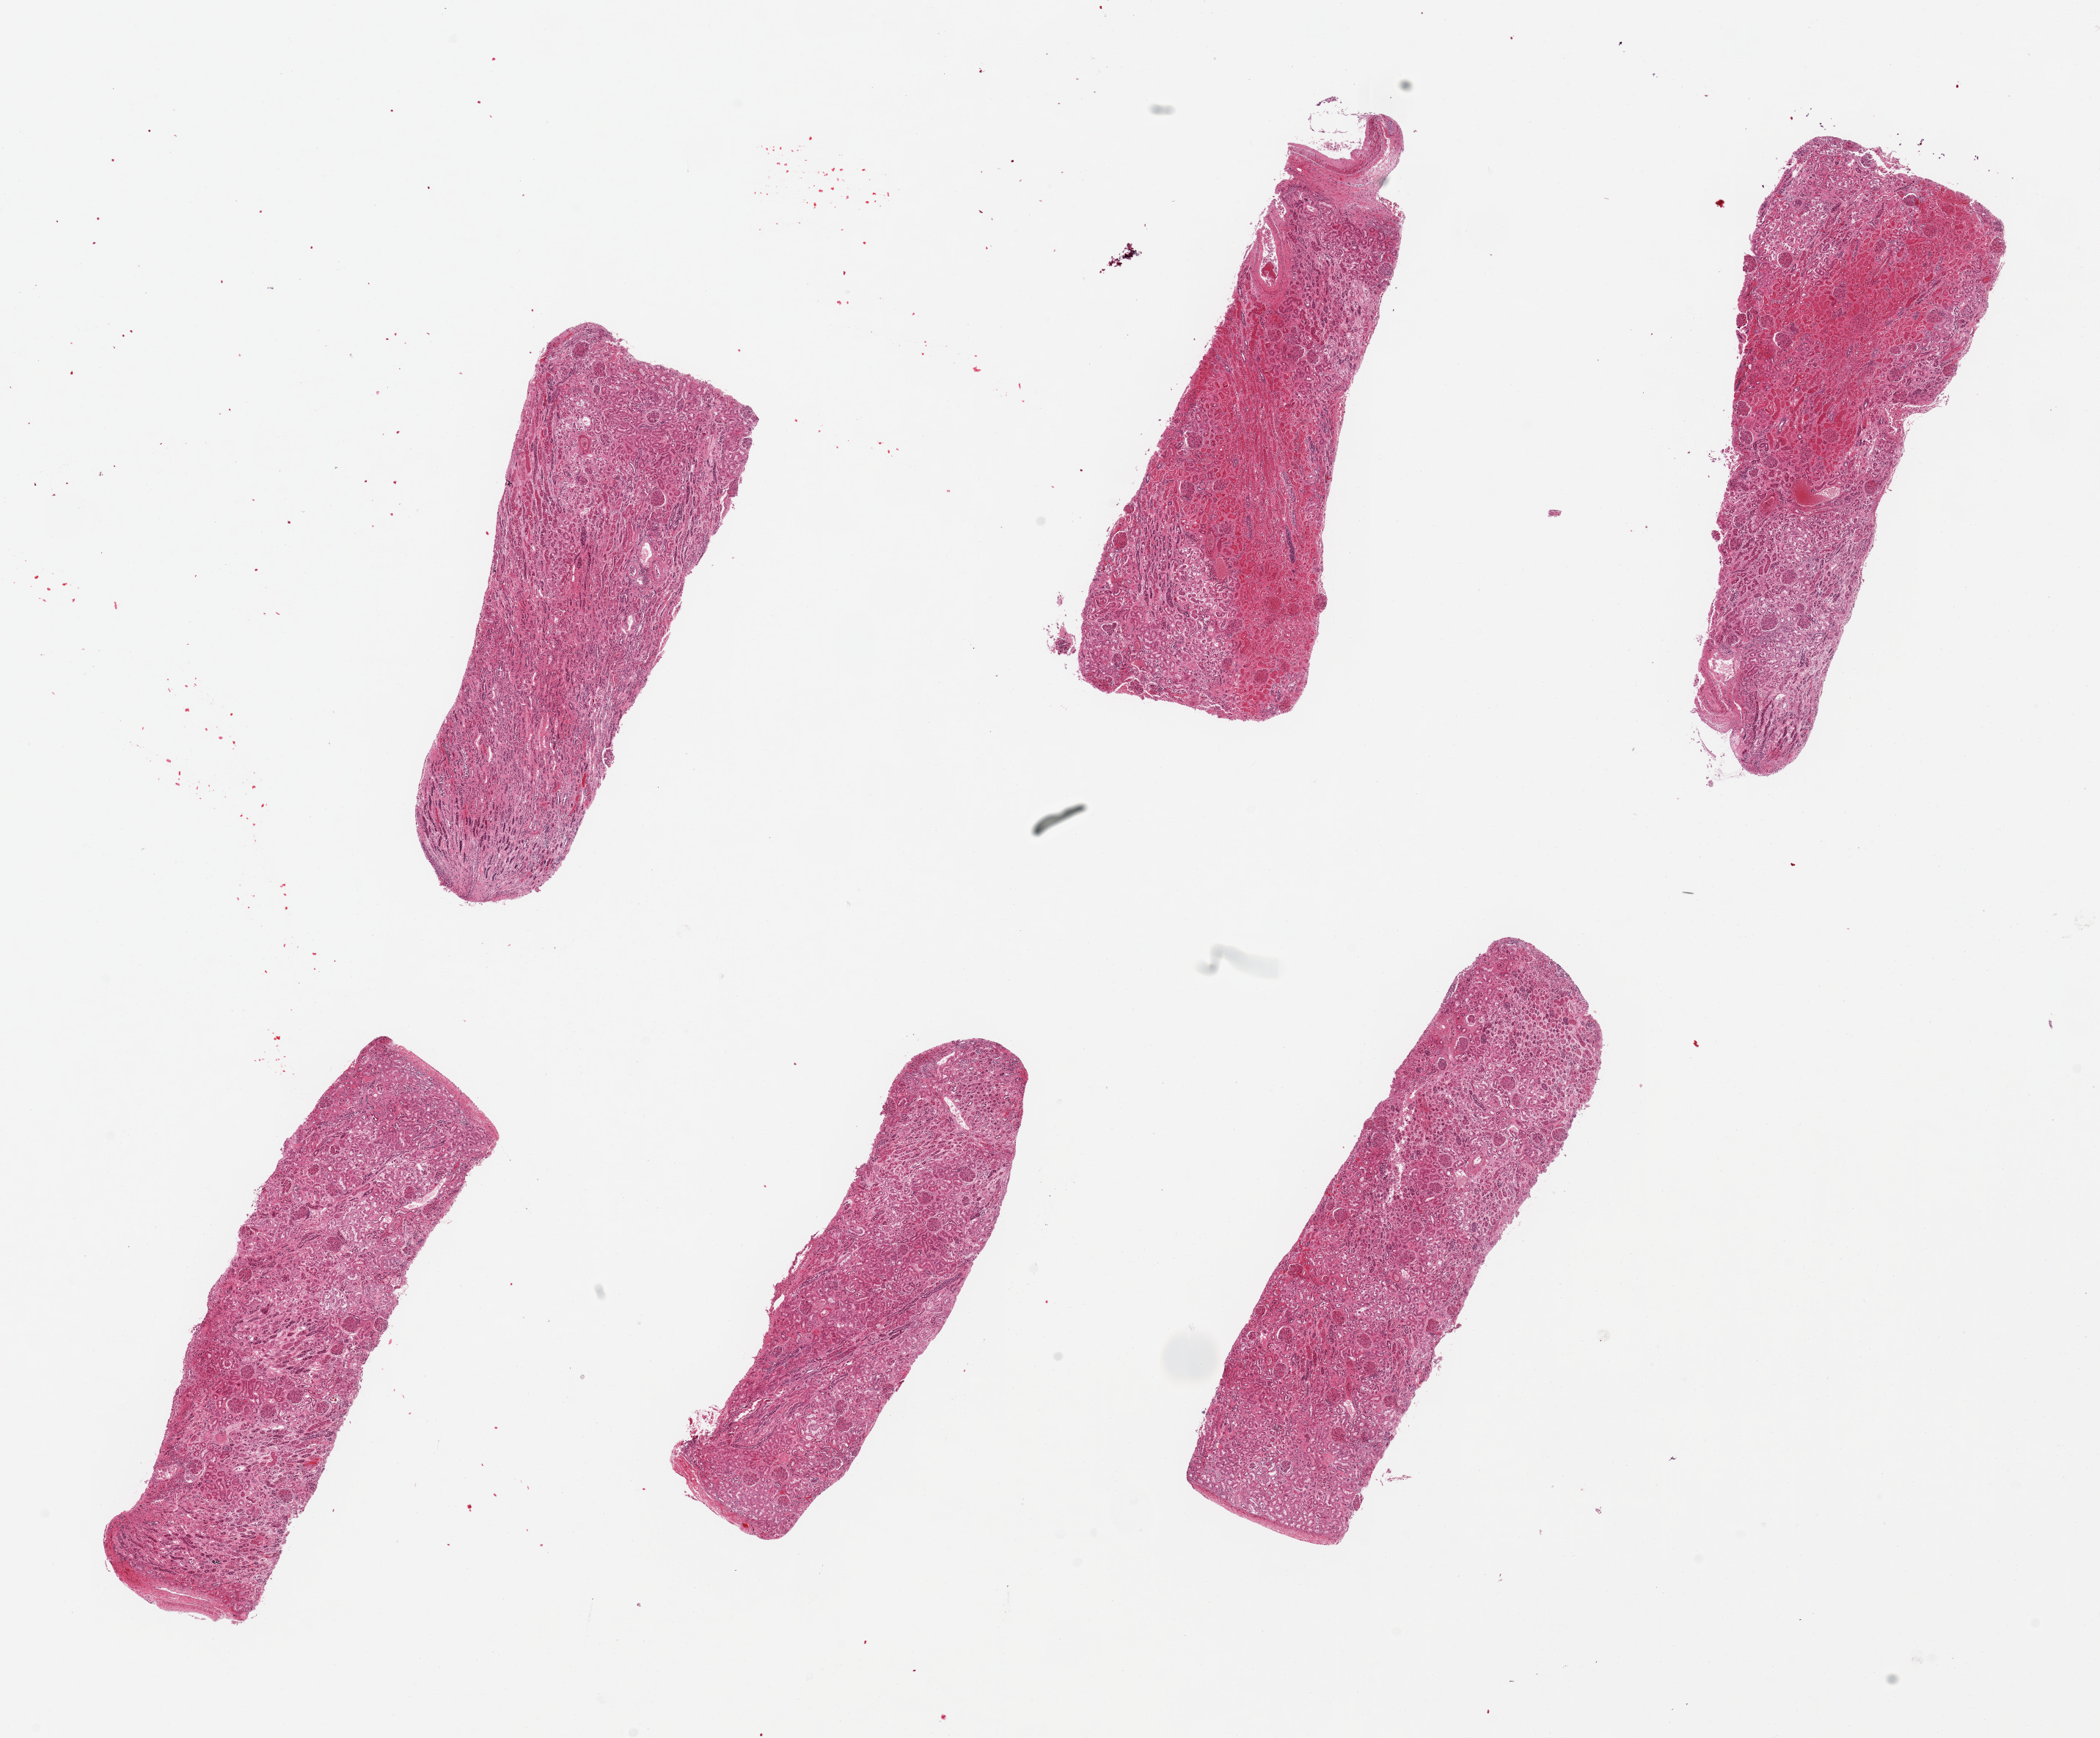
Digitized haematoxylin and eosin-stained section — shown as a low-resolution overview of the whole scanned area (about 22.6 x 18.7 mm). PAXgene-fixed, paraffin-embedded tissue. Sampled site (target tissue): renal cortex. Donor tissue sample. Female donor.
• reviewer comment on this tissue sample: 6 pieces, up to 6.5x2mm; 5 with cortex (2 of which have infarcts); 1 has cortex and medulla. No chronic lesions